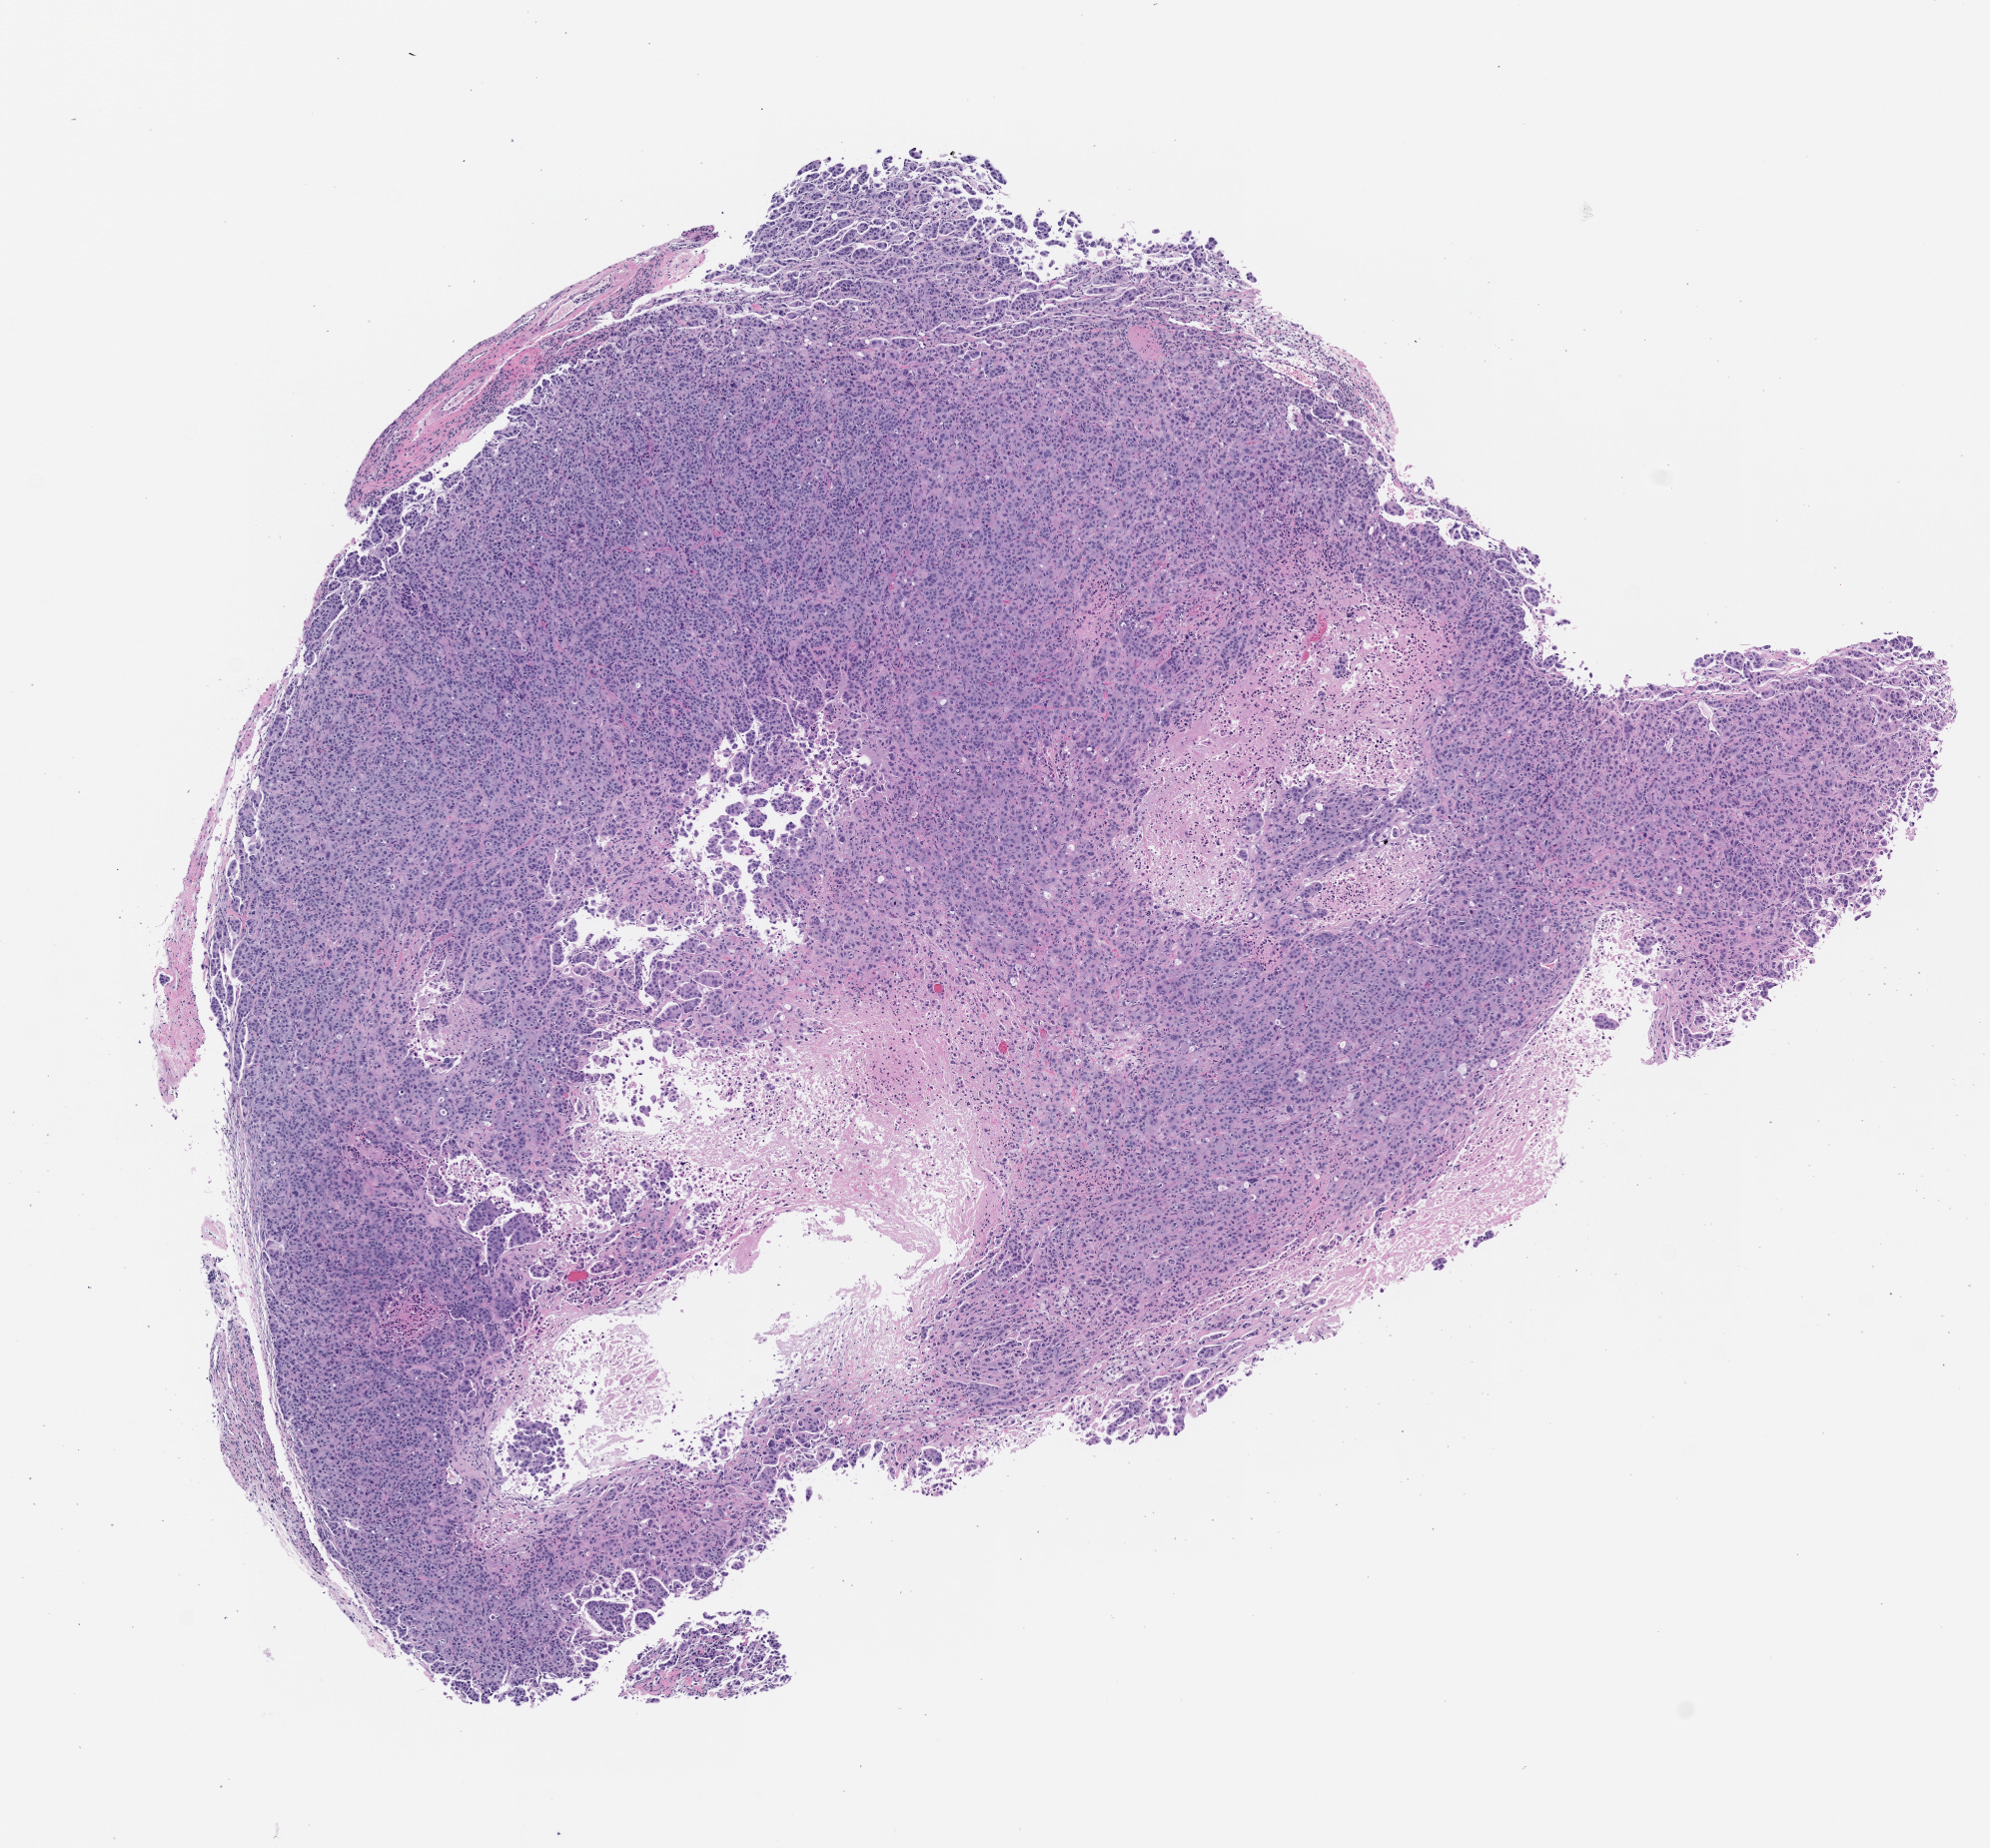
Hematoxylin and eosin (H&E) whole-slide image of a patient-derived xenograft (PDX) tumor grown in a mouse, shown as a low-resolution overview of the whole scanned area (about 8.0 x 7.4 mm), FFPE section, originating tumor site category: lung.
* originating patient diagnosis: Lung Squamous Cell Carcinoma